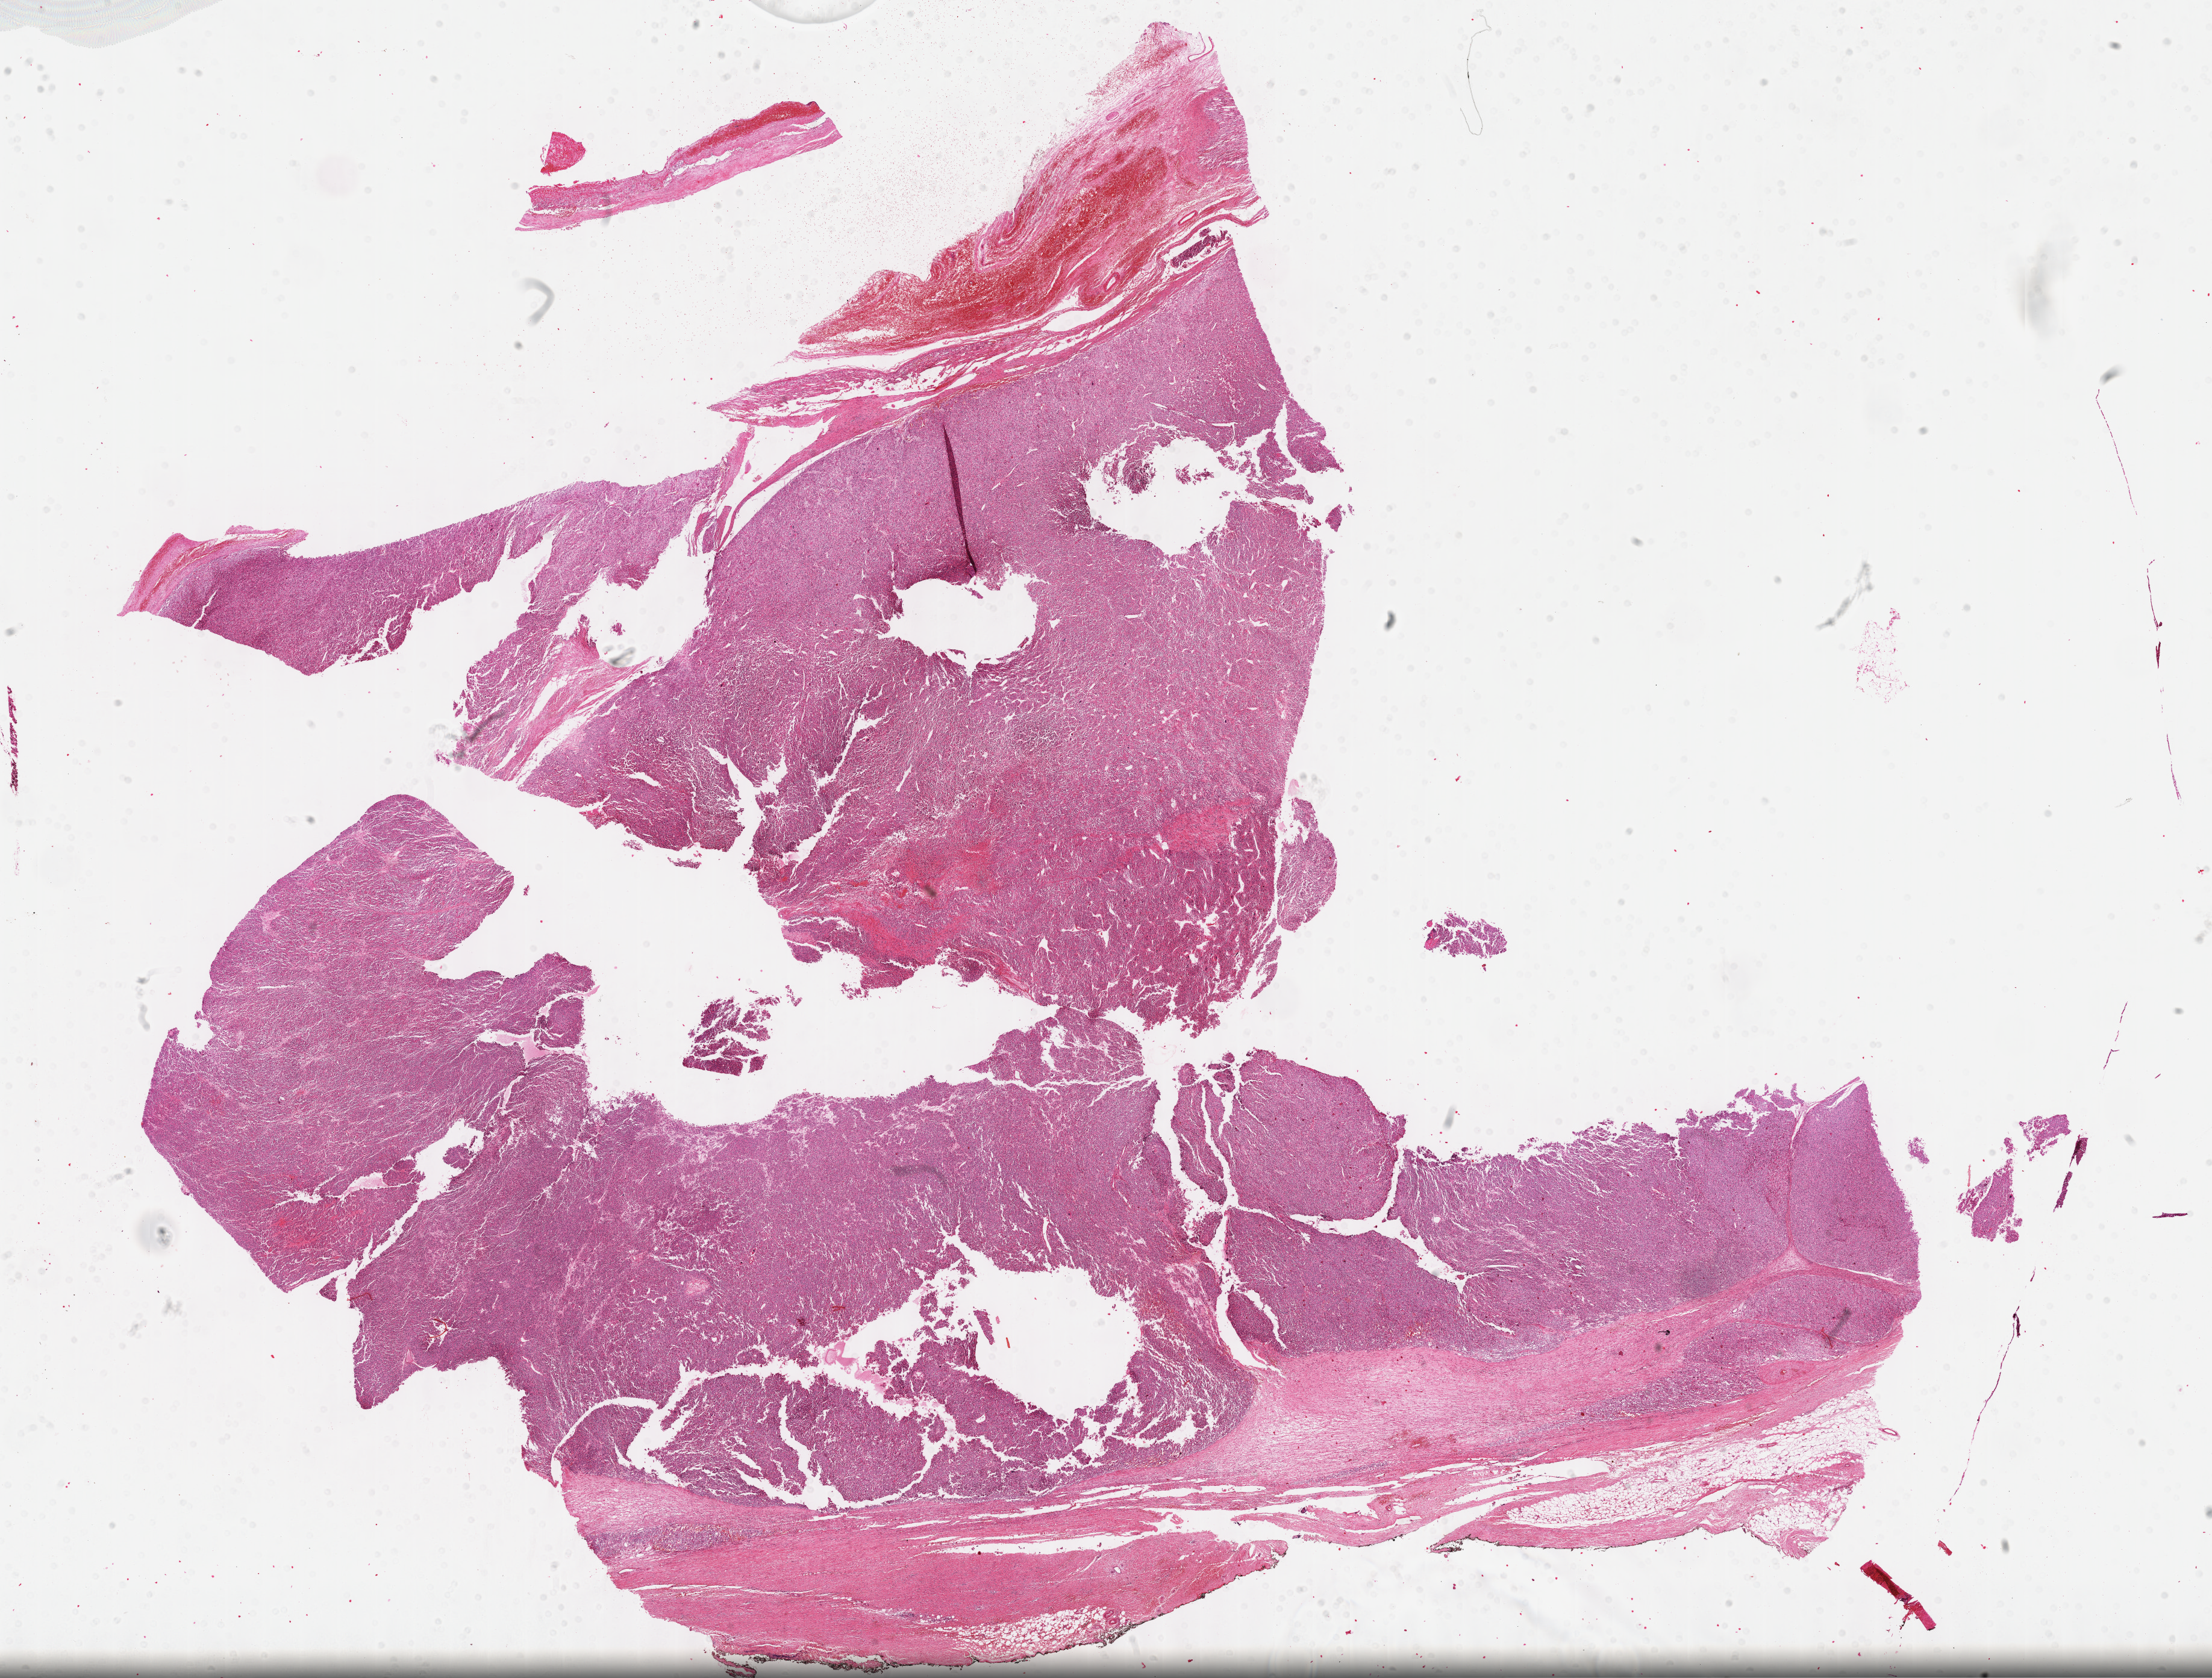
Digitized Hematoxylin and eosin (H&E) stained tissue section (whole slide), low-resolution overview of the scanned area, about 29.7 x 22.5 mm (acquisition: 40x scan); formalin-fixed paraffin-embedded (FFPE) diagnostic section; adrenal cortex, primary tumour sample. Male, age 30 years at initial diagnosis.
Pathologic diagnosis: Adrenal cortical carcinoma (cortex of adrenal gland).